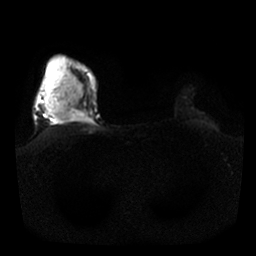
Breast MRI, one axial slice. Slice 22 of 25 in the series (ordered by position). Diffusion-weighted series; image 2 of 4 stored at this slice position (different b-values; order by instance number). 1.5 T. 4 mm slice thickness. 256 × 256 image matrix. Female patient.
Annotated regions visible in this slice (outlined manually by an expert reader):
- tumour on diffusion-weighted imaging: bounding box [x1, y1, x2, y2] px = [44, 56, 86, 118]